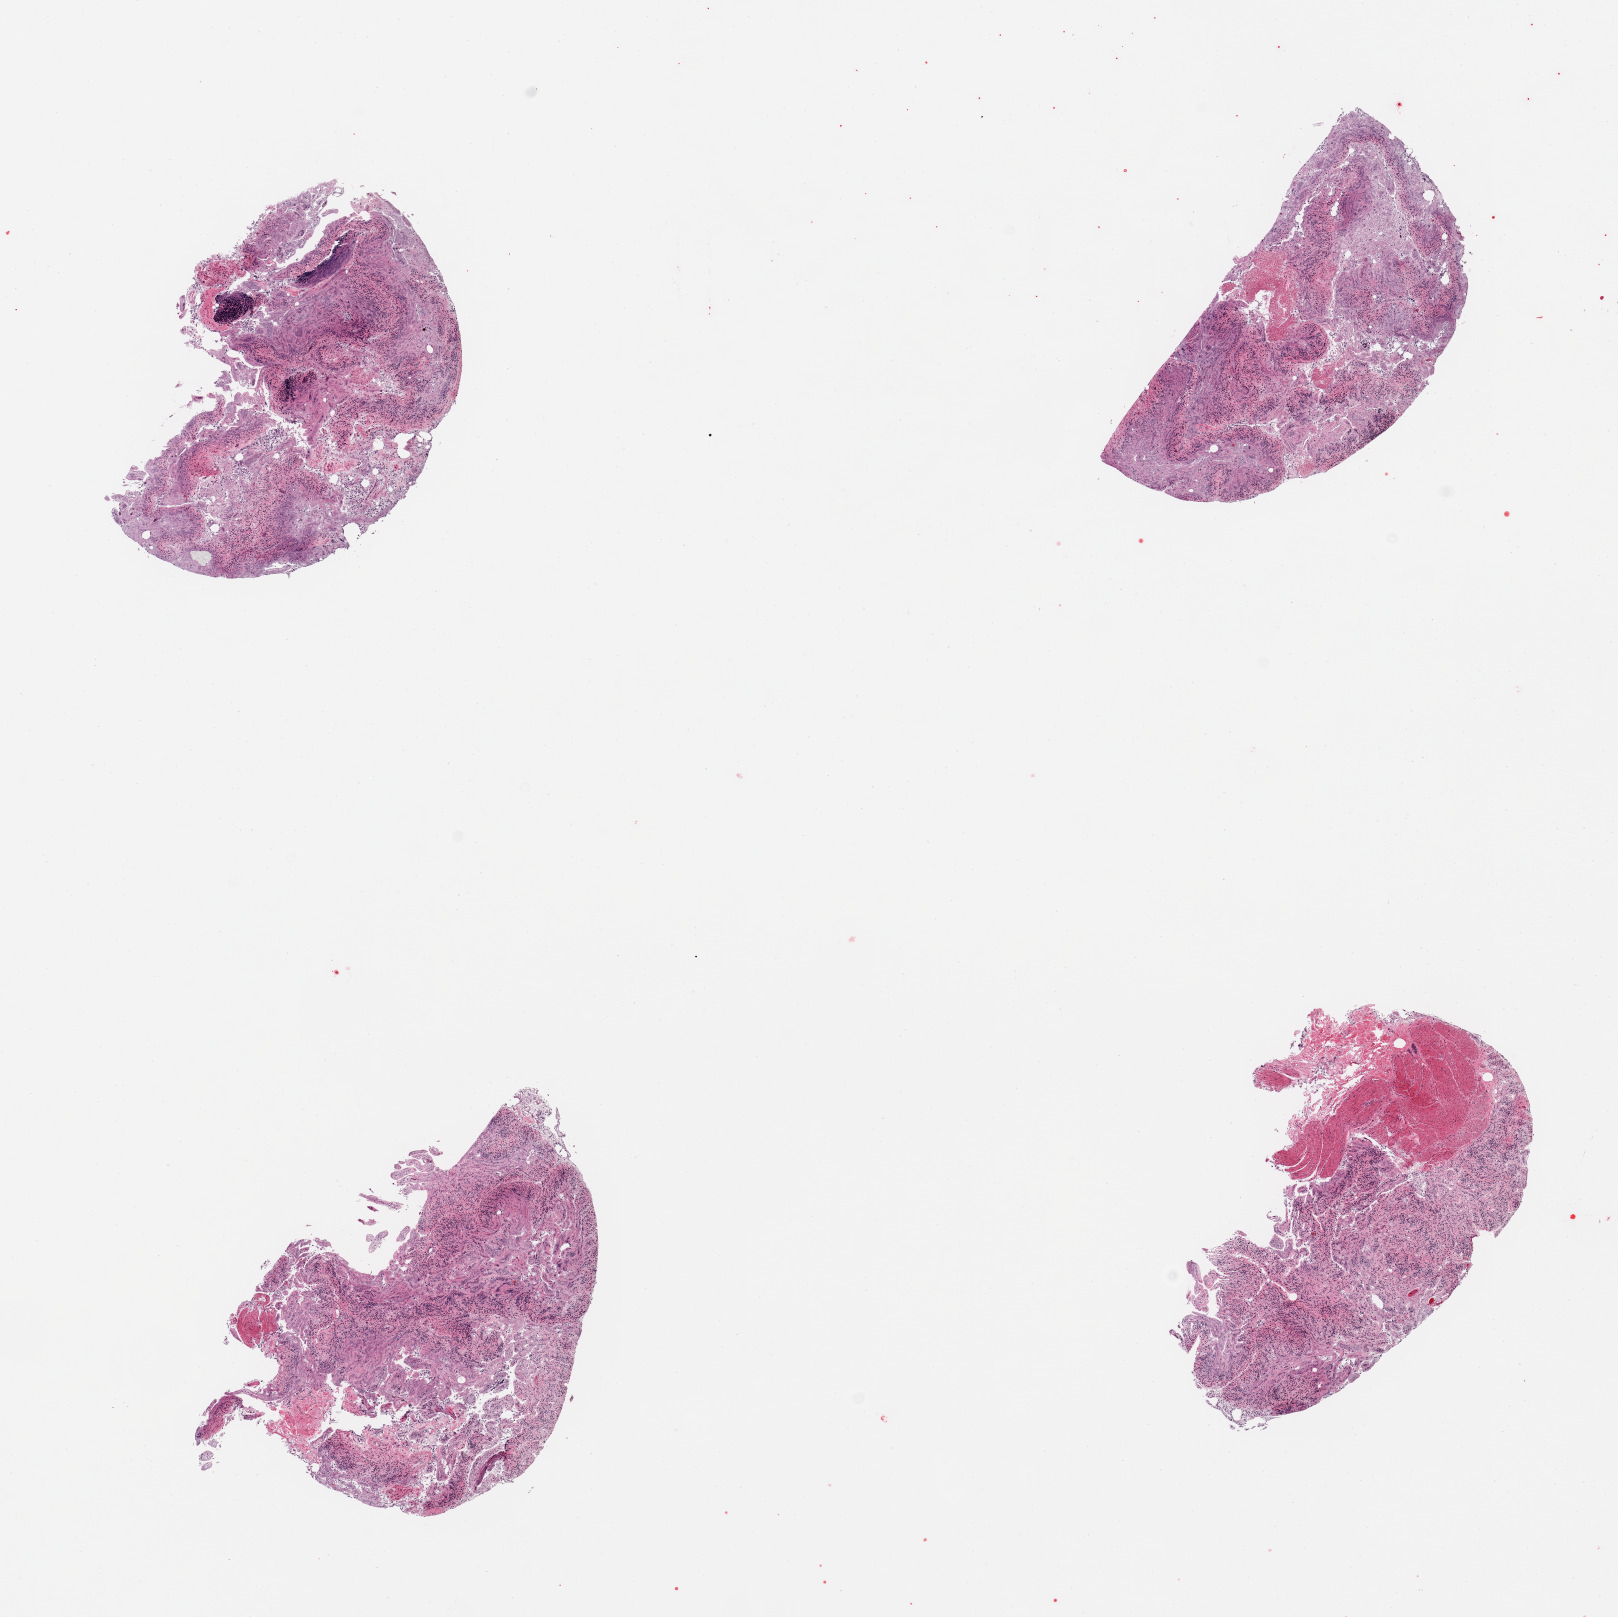
Digitized haematoxylin and eosin-stained section — shown as a low-resolution overview of the whole scanned area (about 12.8 x 12.8 mm, acquisition: 20x scan); PAXgene-fixed paraffin-embedded (PFPE) section; section of ileum (target tissue); tissue donor sample. Male donor.
Pathologist's review note for this sample: 4 pieces; autolyzed mucosa and only focal lymphoid aggregate; small fragments of muscularis (not target).